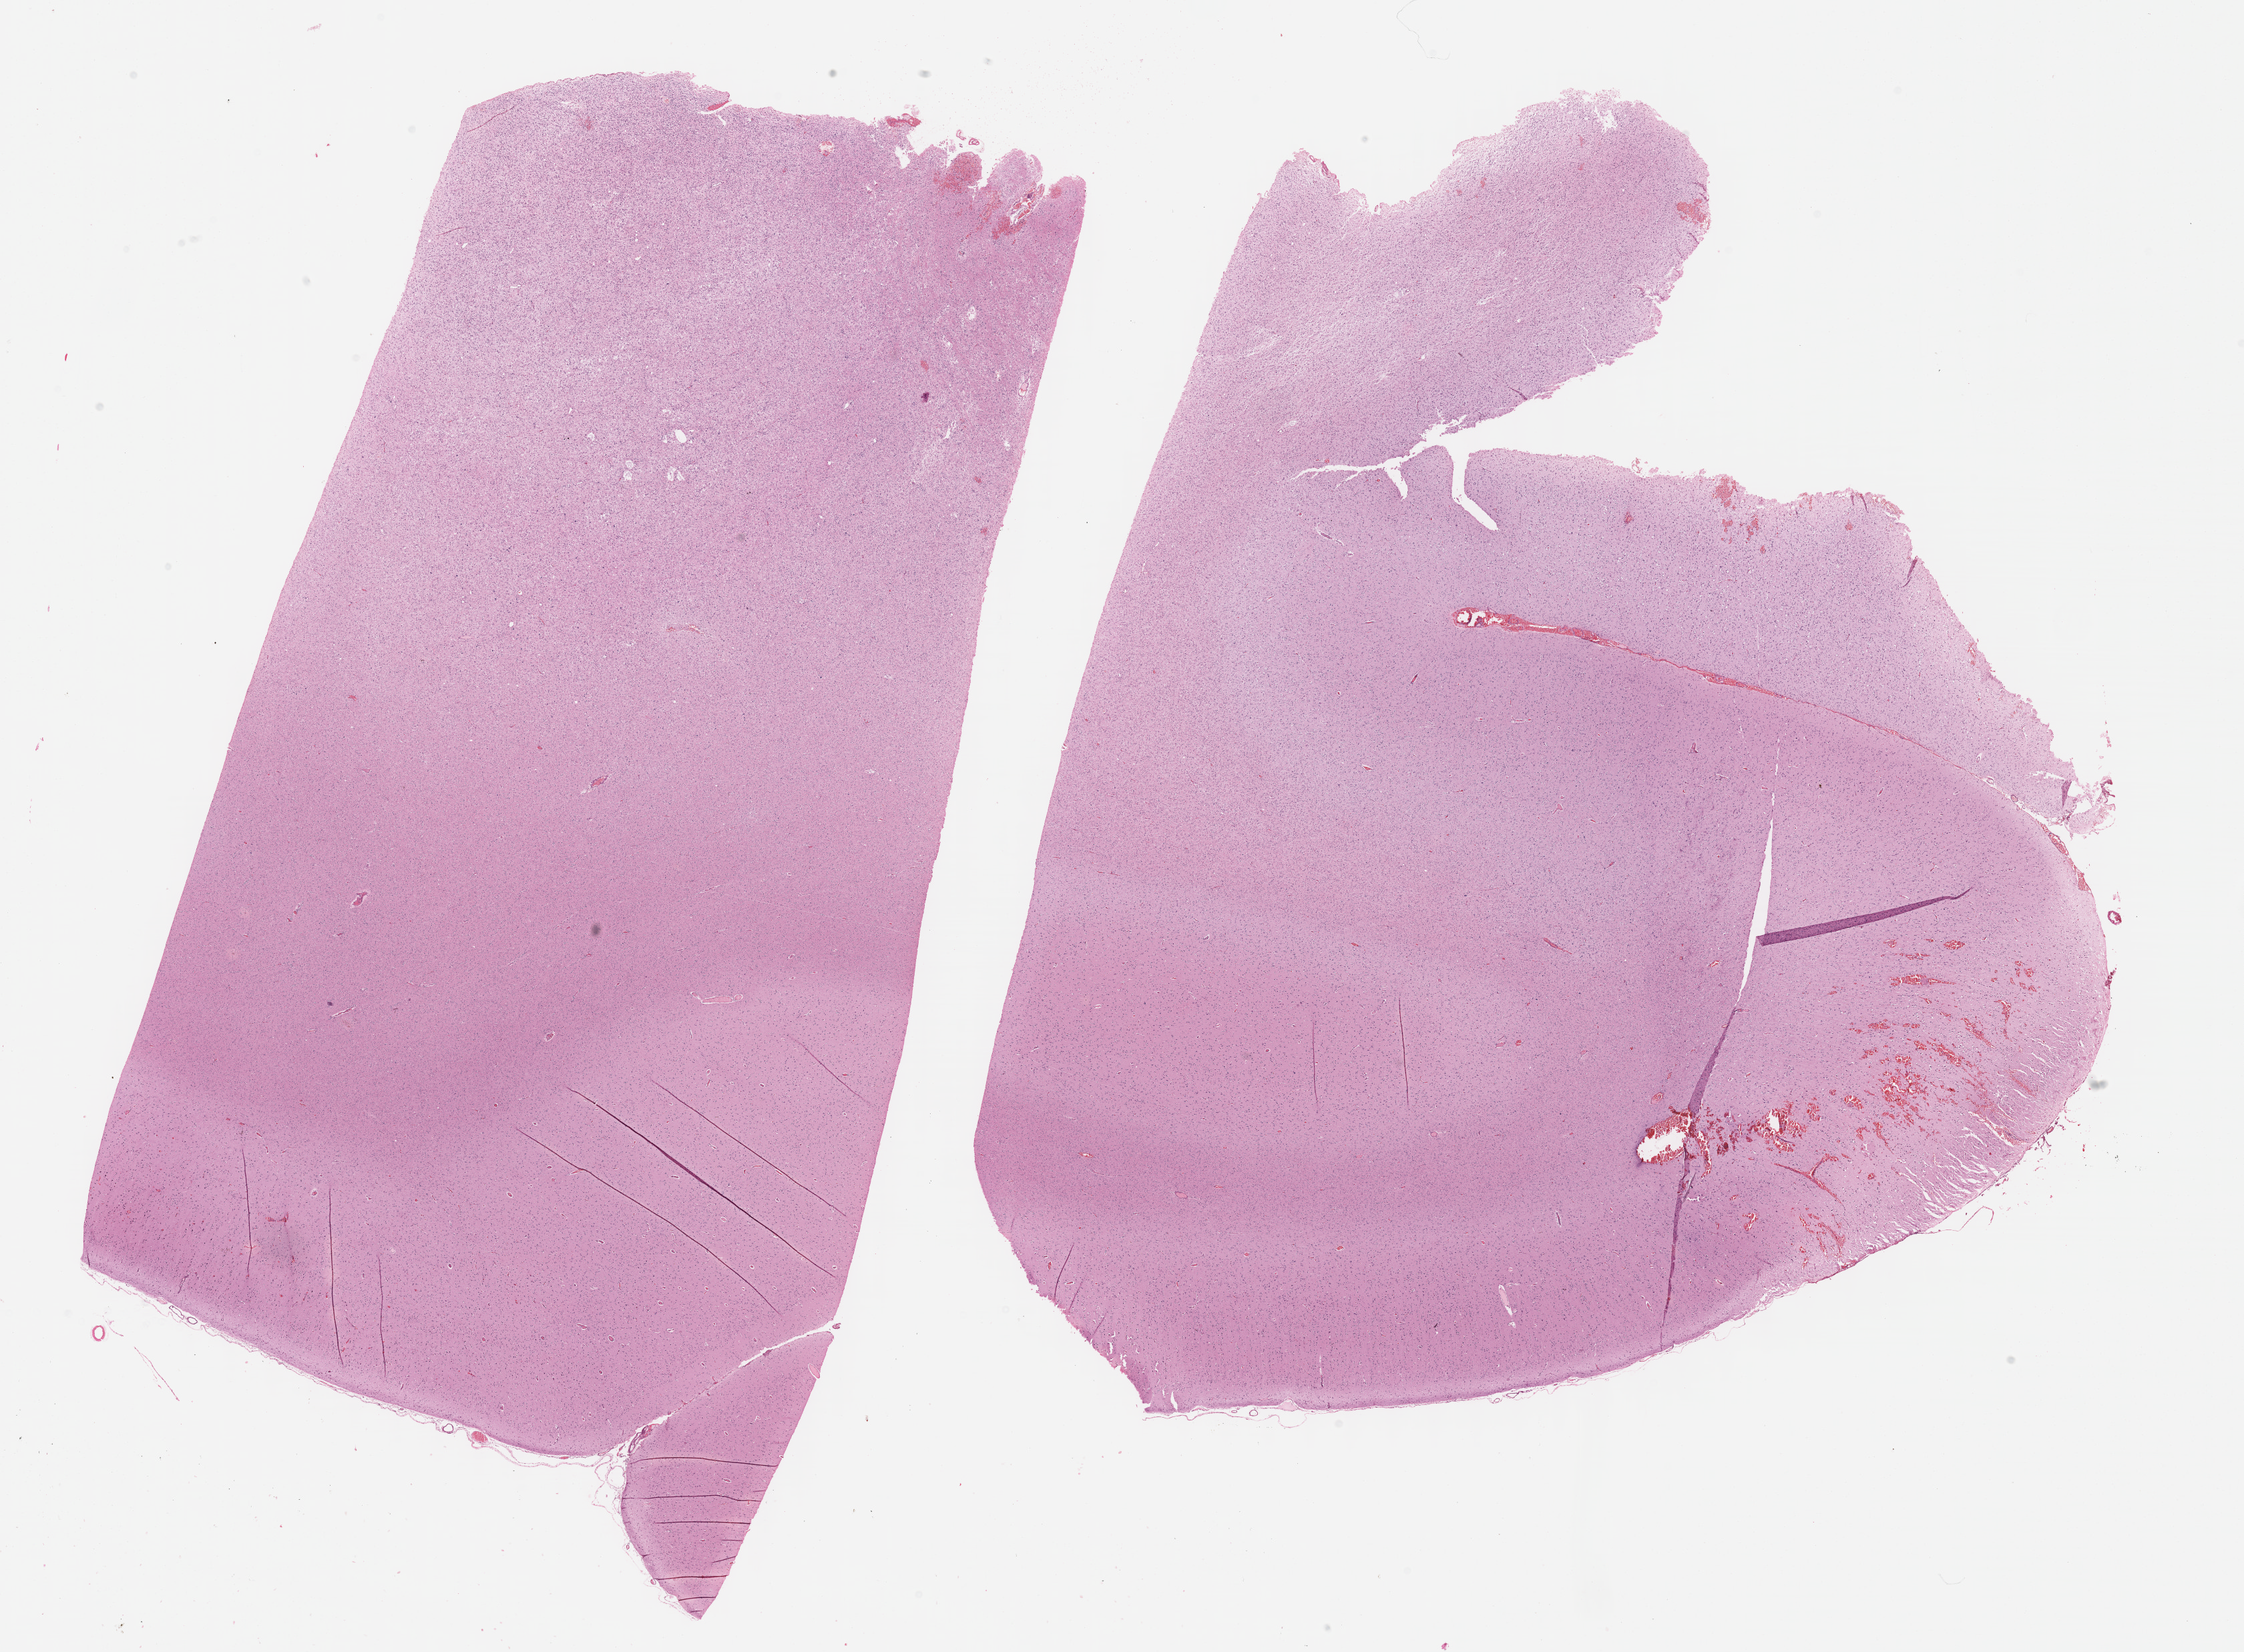
Digitized H&E tissue section (whole slide) — shown as a low-resolution overview of the whole scanned area (about 27.2 x 20.0 mm), formalin-fixed paraffin-embedded (FFPE) diagnostic section, sample: primary tumour, brain. Male, age 39 years at initial diagnosis. Histologic grade: G2 (moderately differentiated).
Laterality: right. Pathologic diagnosis: Mixed glioma.